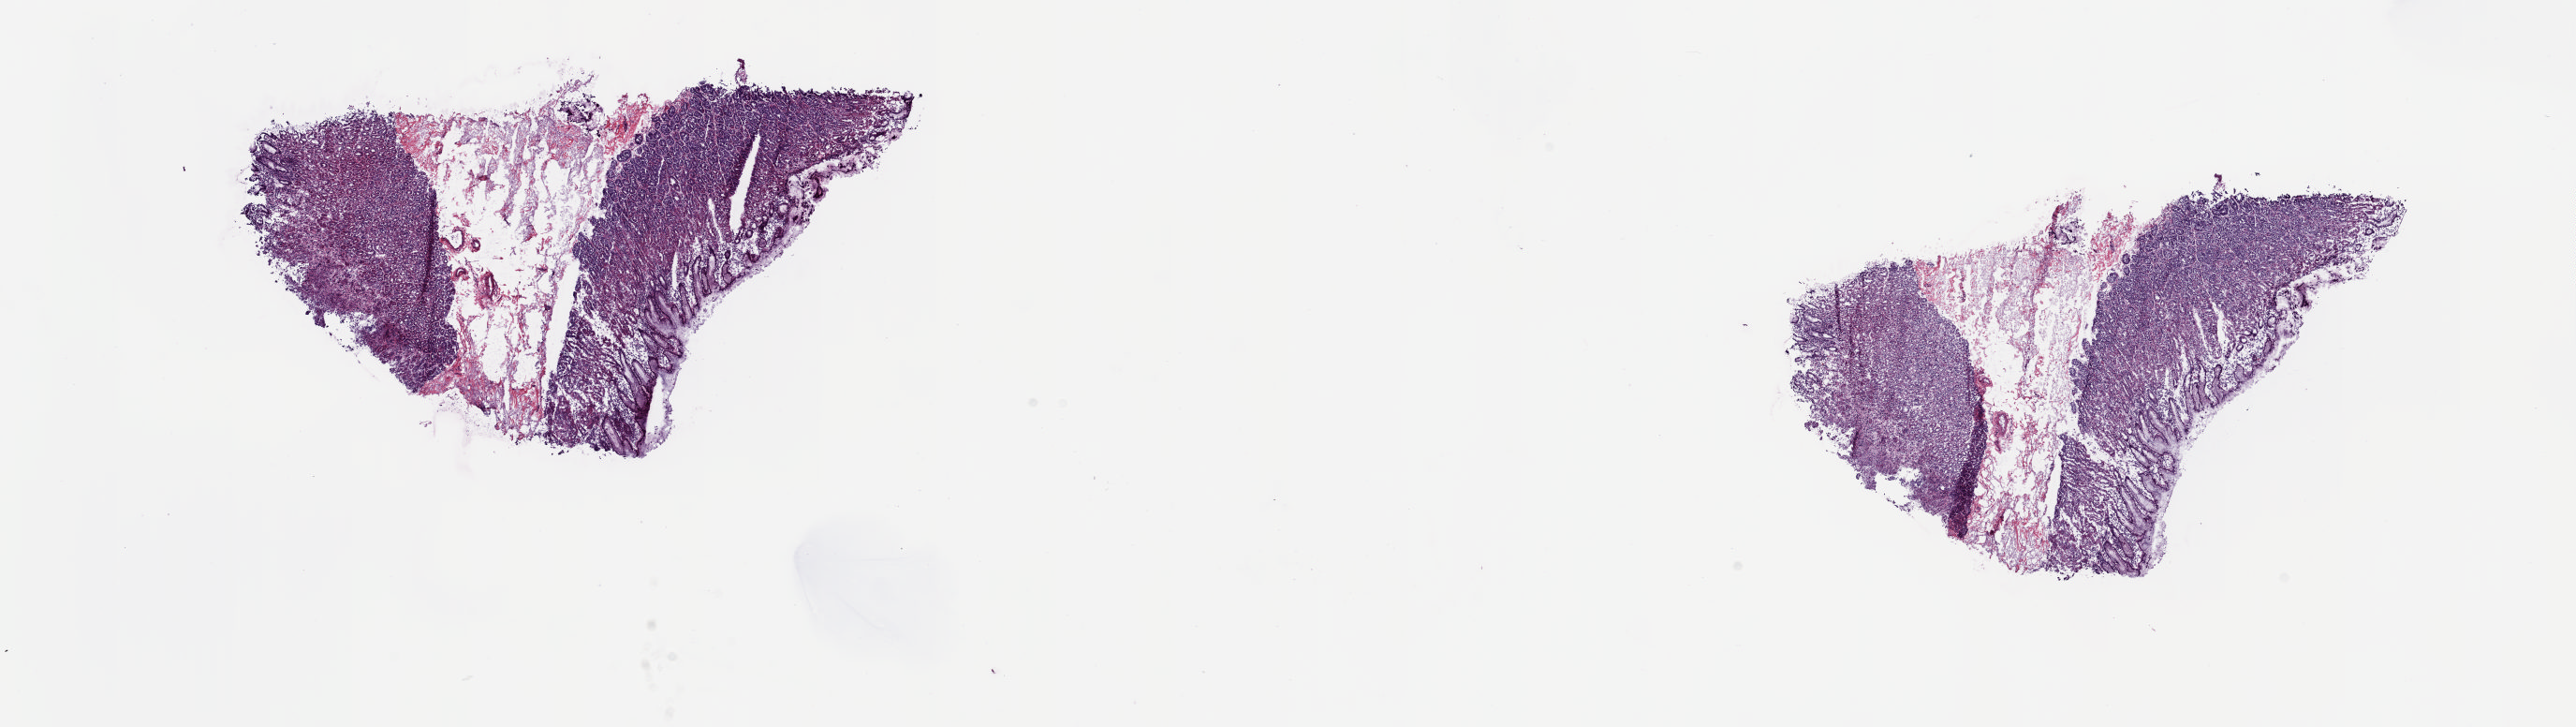
Whole-slide histology image, H&E-stained, low-resolution overview of the scanned area, about 21.8 x 6.2 mm (acquisition: 20x scan); frozen section from the top of the tissue portion; sample: solid tissue normal (non-tumour tissue), esophagus. Patient: male, age at initial diagnosis 57 years. Composition of this section per pathologist review: tumour cells 0%, tumour nuclei 0%, normal cells 60%, stromal cells 40%, necrosis 0%. Inflammatory infiltration, as recorded: lymphocyte infiltration 40%, monocyte infiltration 20%, neutrophil infiltration 20%.
- this section: solid tissue normal (non-tumour) sample from the same patient
- patient diagnosis: Adenocarcinoma, NOS (lower third of esophagus)